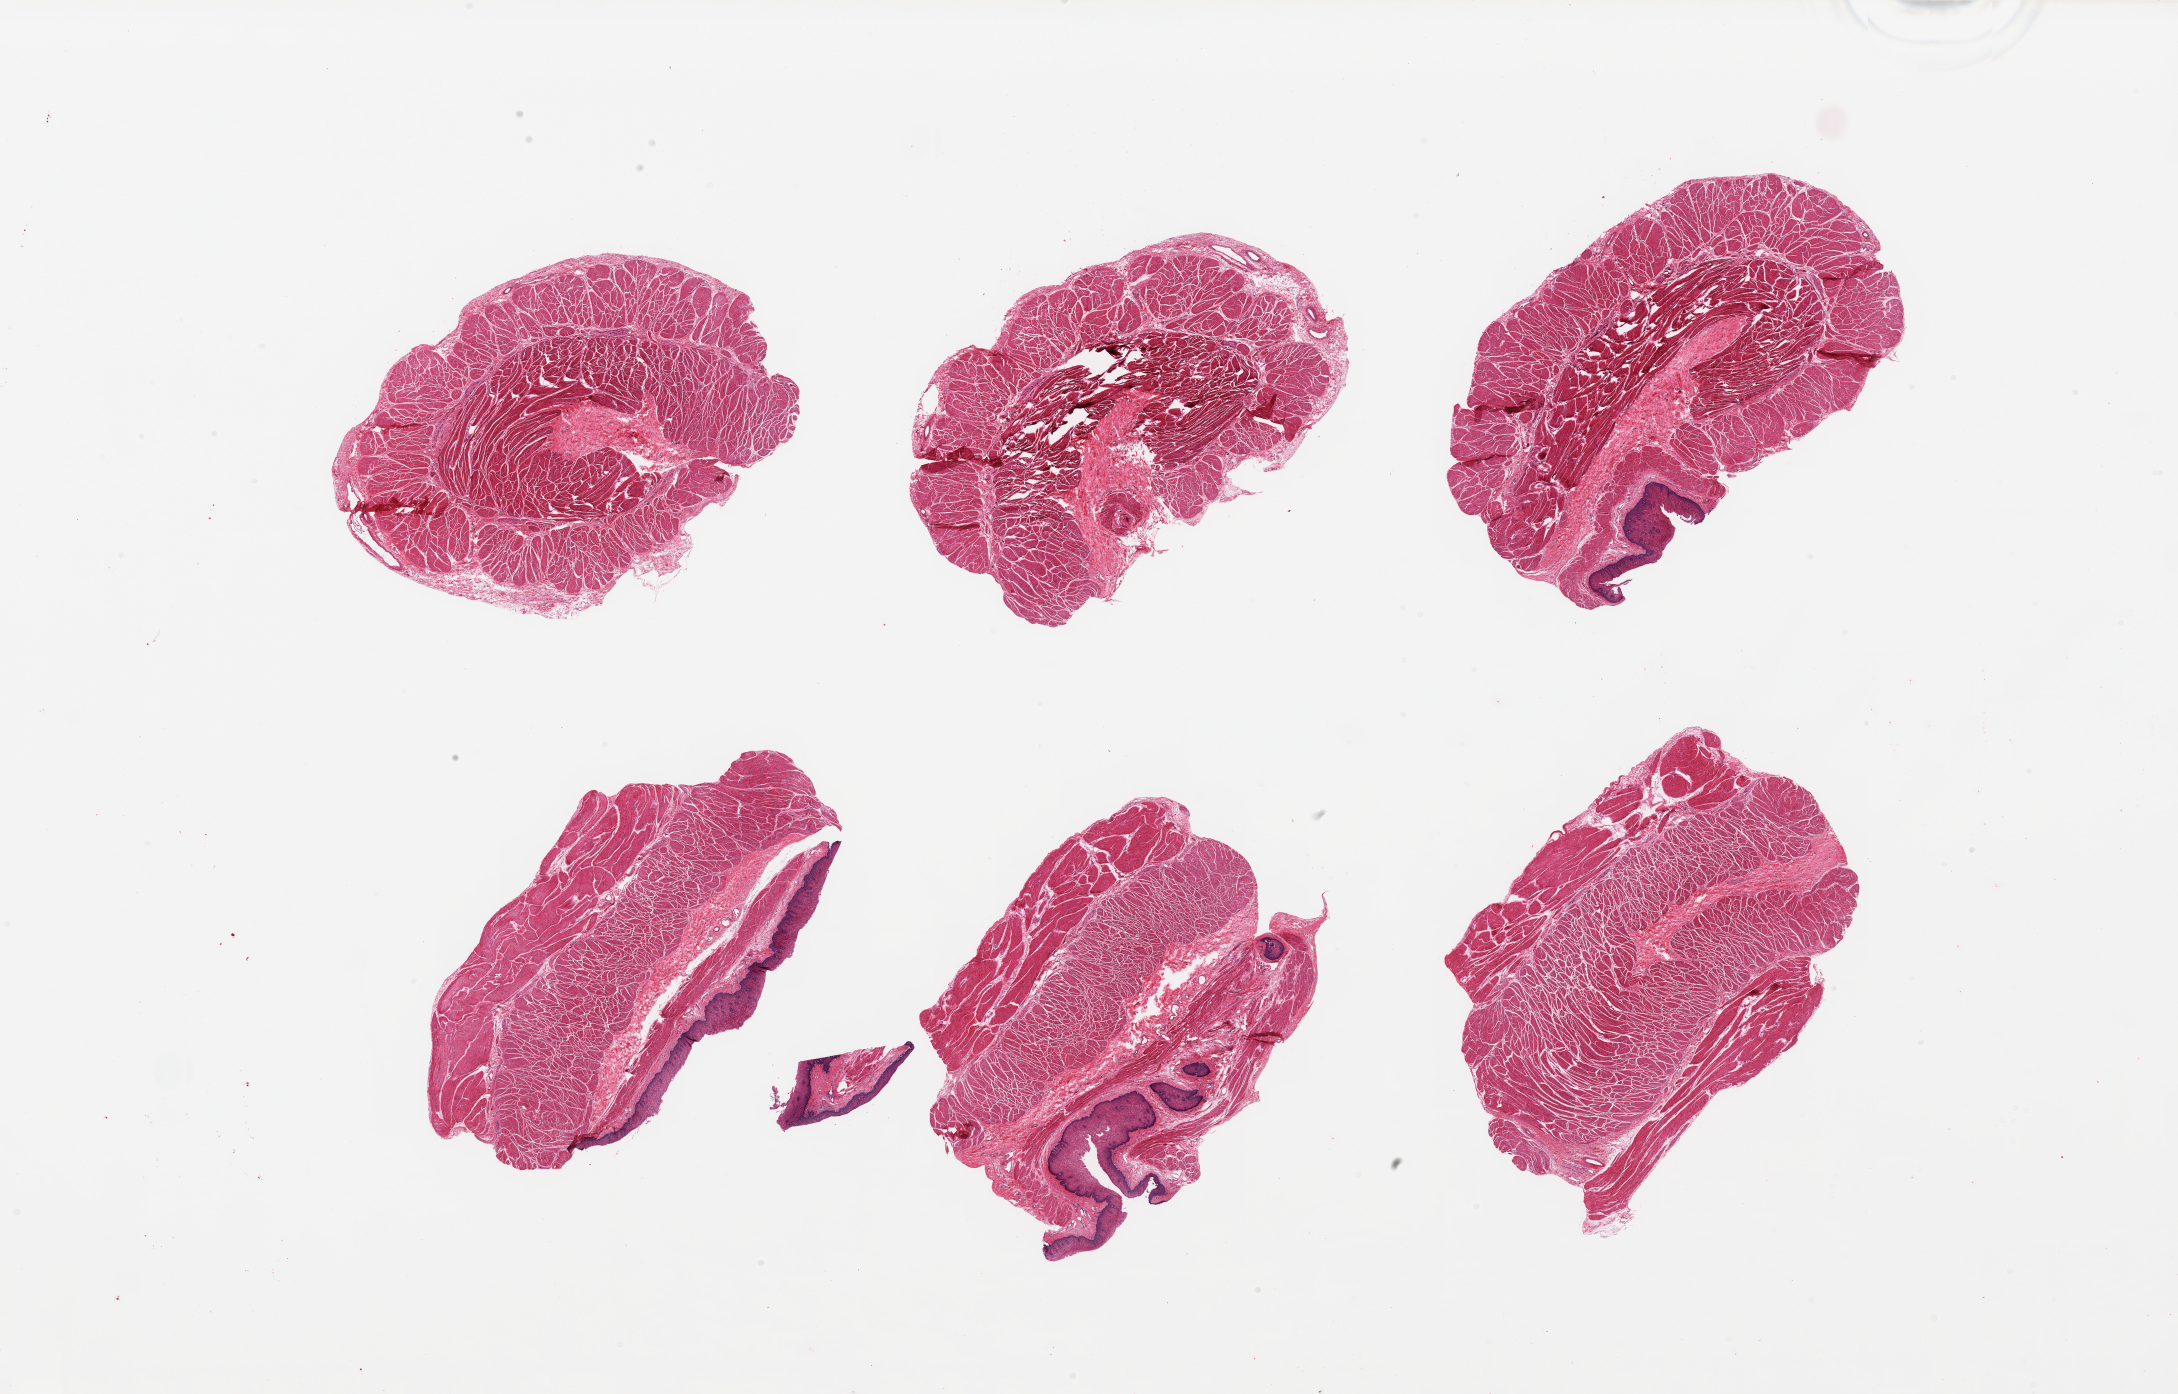
Whole-slide image, haematoxylin and eosin stain, brightfield, shown as a low-resolution overview of the whole scanned area (about 34.5 x 22.1 mm, from a 20x scan). PAXgene-fixed, paraffin-embedded tissue. Section of gastroesophageal junction (target tissue). Donor tissue sample. Donor: female.
• review note (as recorded): 6 pieces; target muscularis, but 3 pieces and detached fragment include squamous mucosa